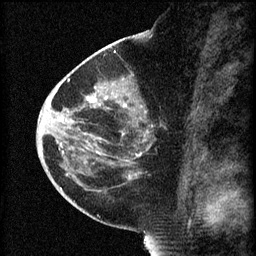
Breast MRI (dynamic contrast-enhanced), one sagittal slice. Slice 32 of 60 in the series (ordered by position). 3 images stored at this slice position (order not interpretable as contrast timing). 1.5 T. TE 4.2 ms, TR 8.2 ms. 2 mm slice thickness. 256 × 256 image matrix. Female patient, age 44 years.
Structures marked on this image (semi-automatic segmentation, software-assisted and operator-edited):
- analysis volume of interest (the breast-tissue region the enhancement analysis was run in; not a lesion): bounding box <73,82,168,165> (left, top, right, bottom; pixels)
- tumour enhancement mask (voxels above the 70 % enhancement threshold inside the analysis volume of interest): <88,96,143,163>